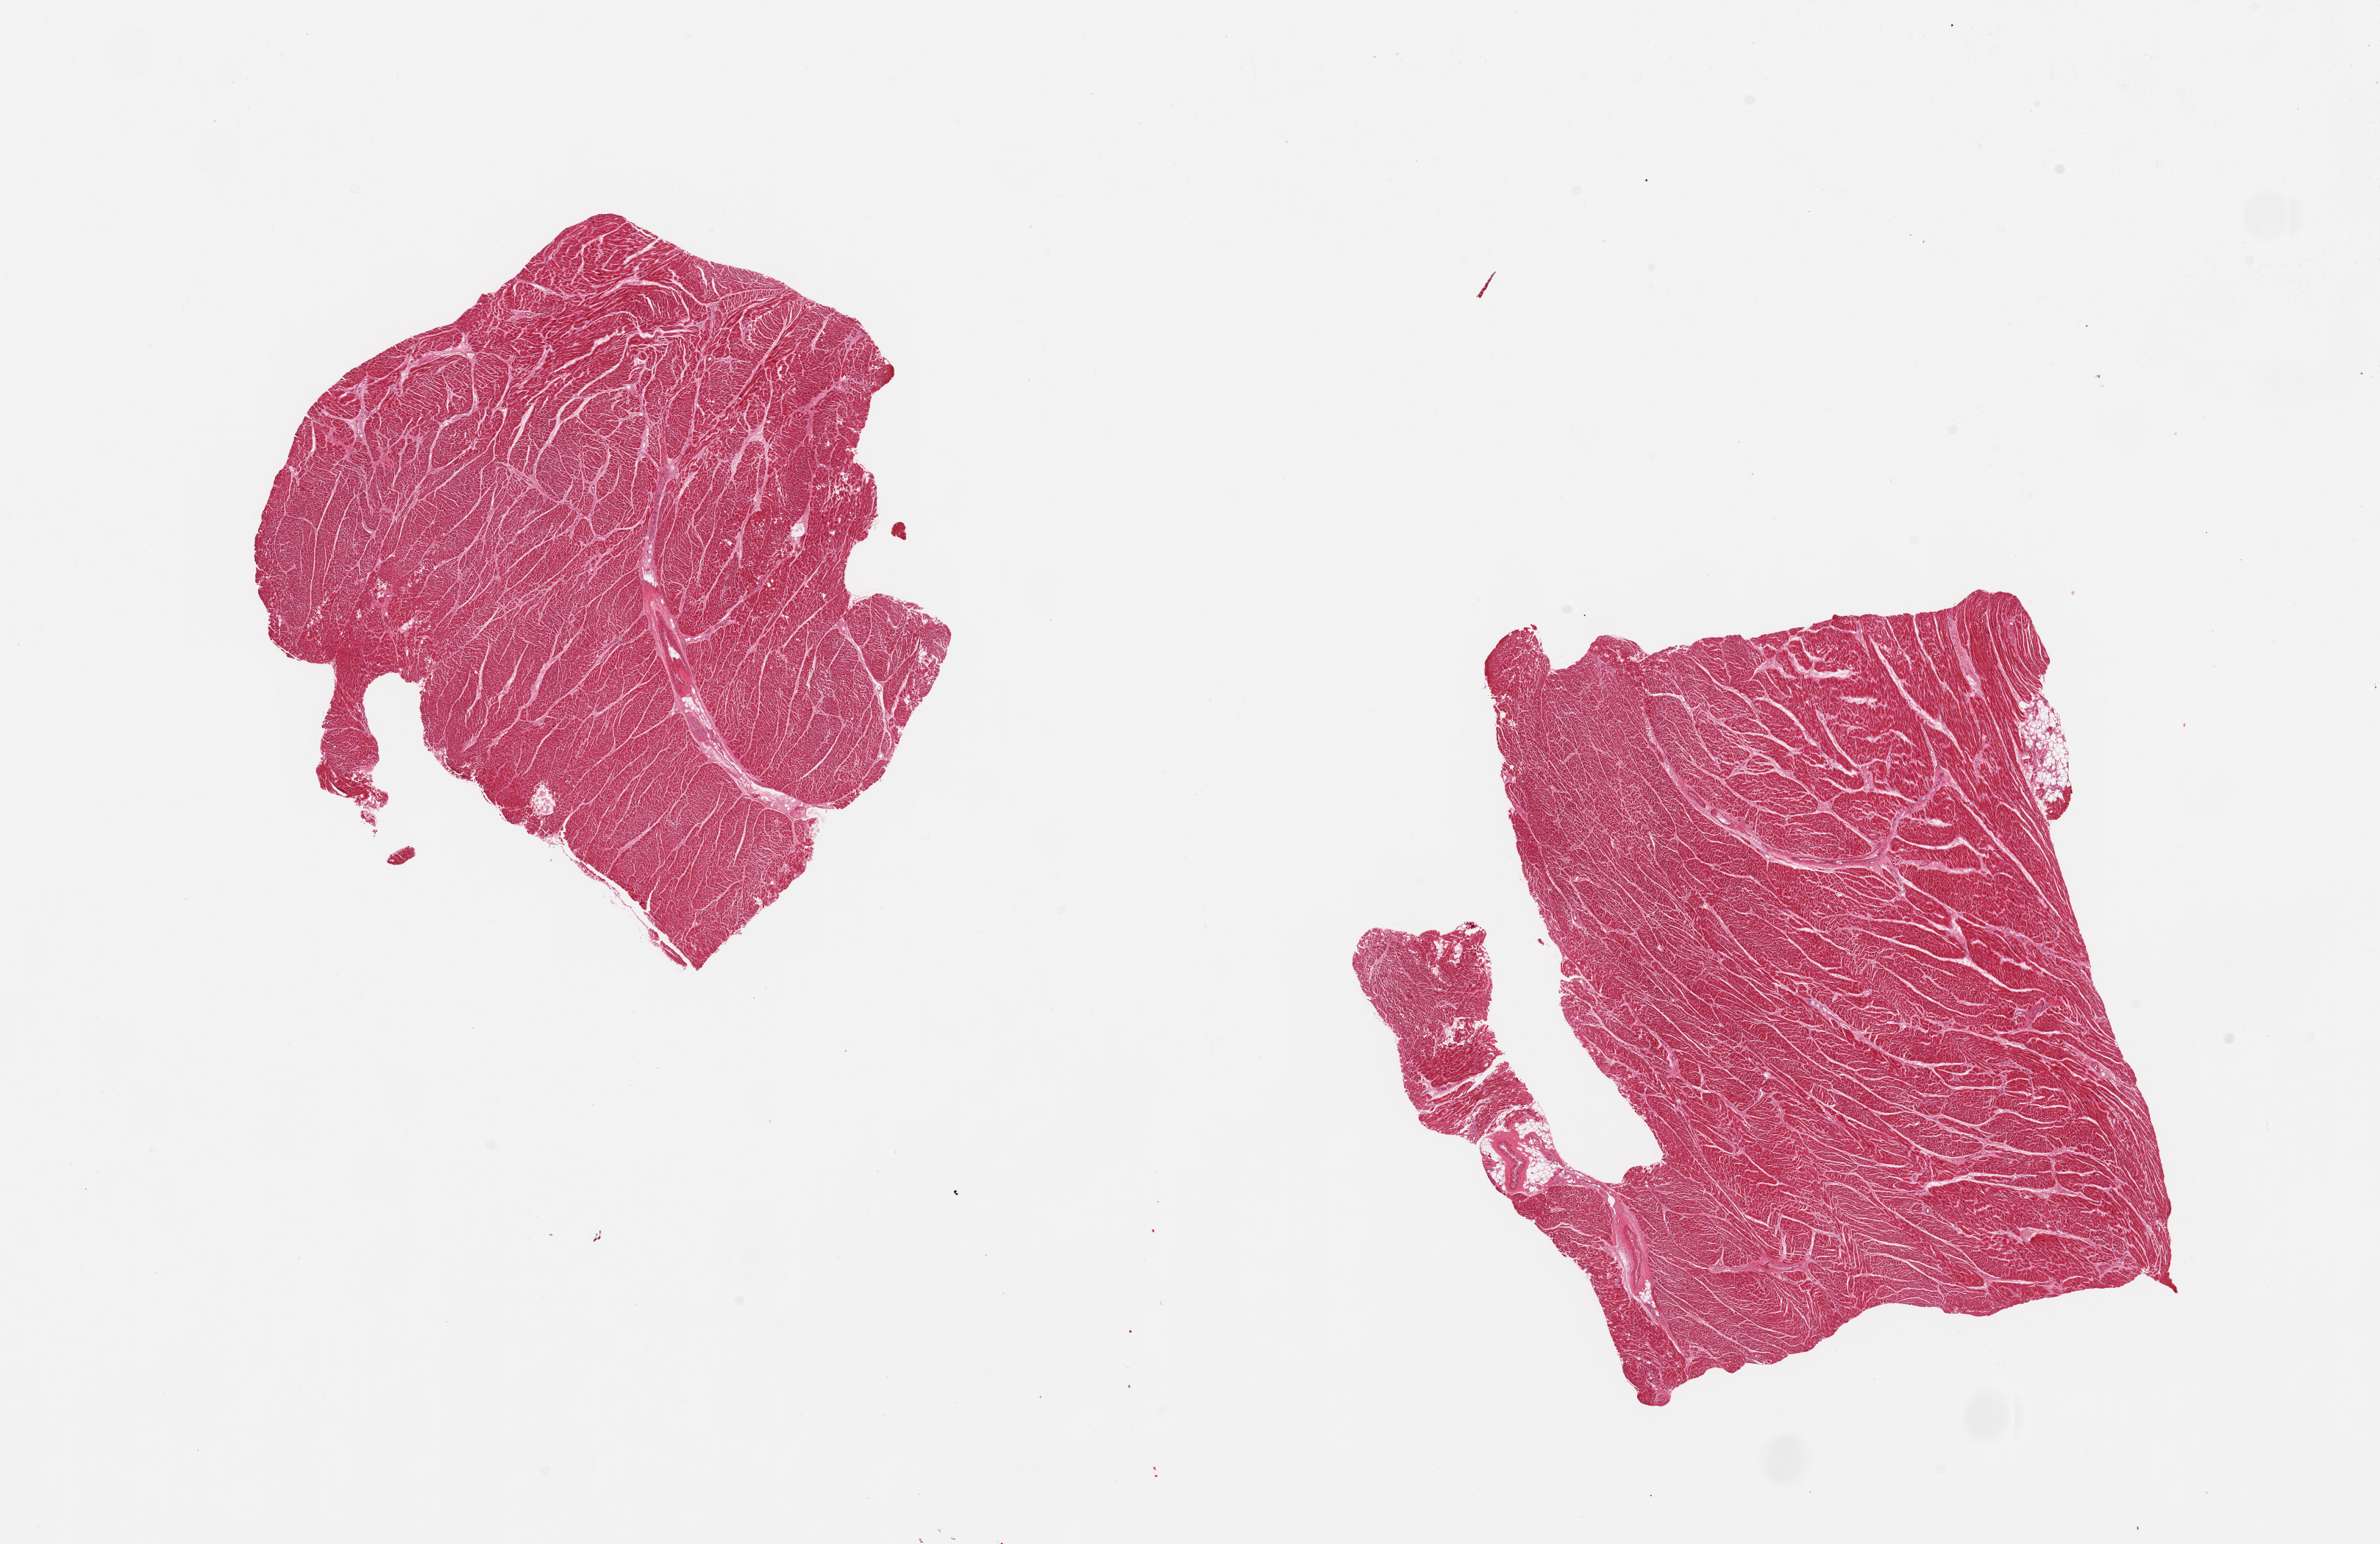
Haematoxylin and eosin whole-slide image, brightfield — whole scanned area (about 25.6 x 16.6 mm, acquisition: 20x scan) shown as a low-resolution overview, PAXgene-fixed paraffin-embedded (PFPE) section, section of heart (target tissue), tissue donor sample. Female donor.
Pathologist's review note for this sample: 2 pieces, minimal ischemic changes.